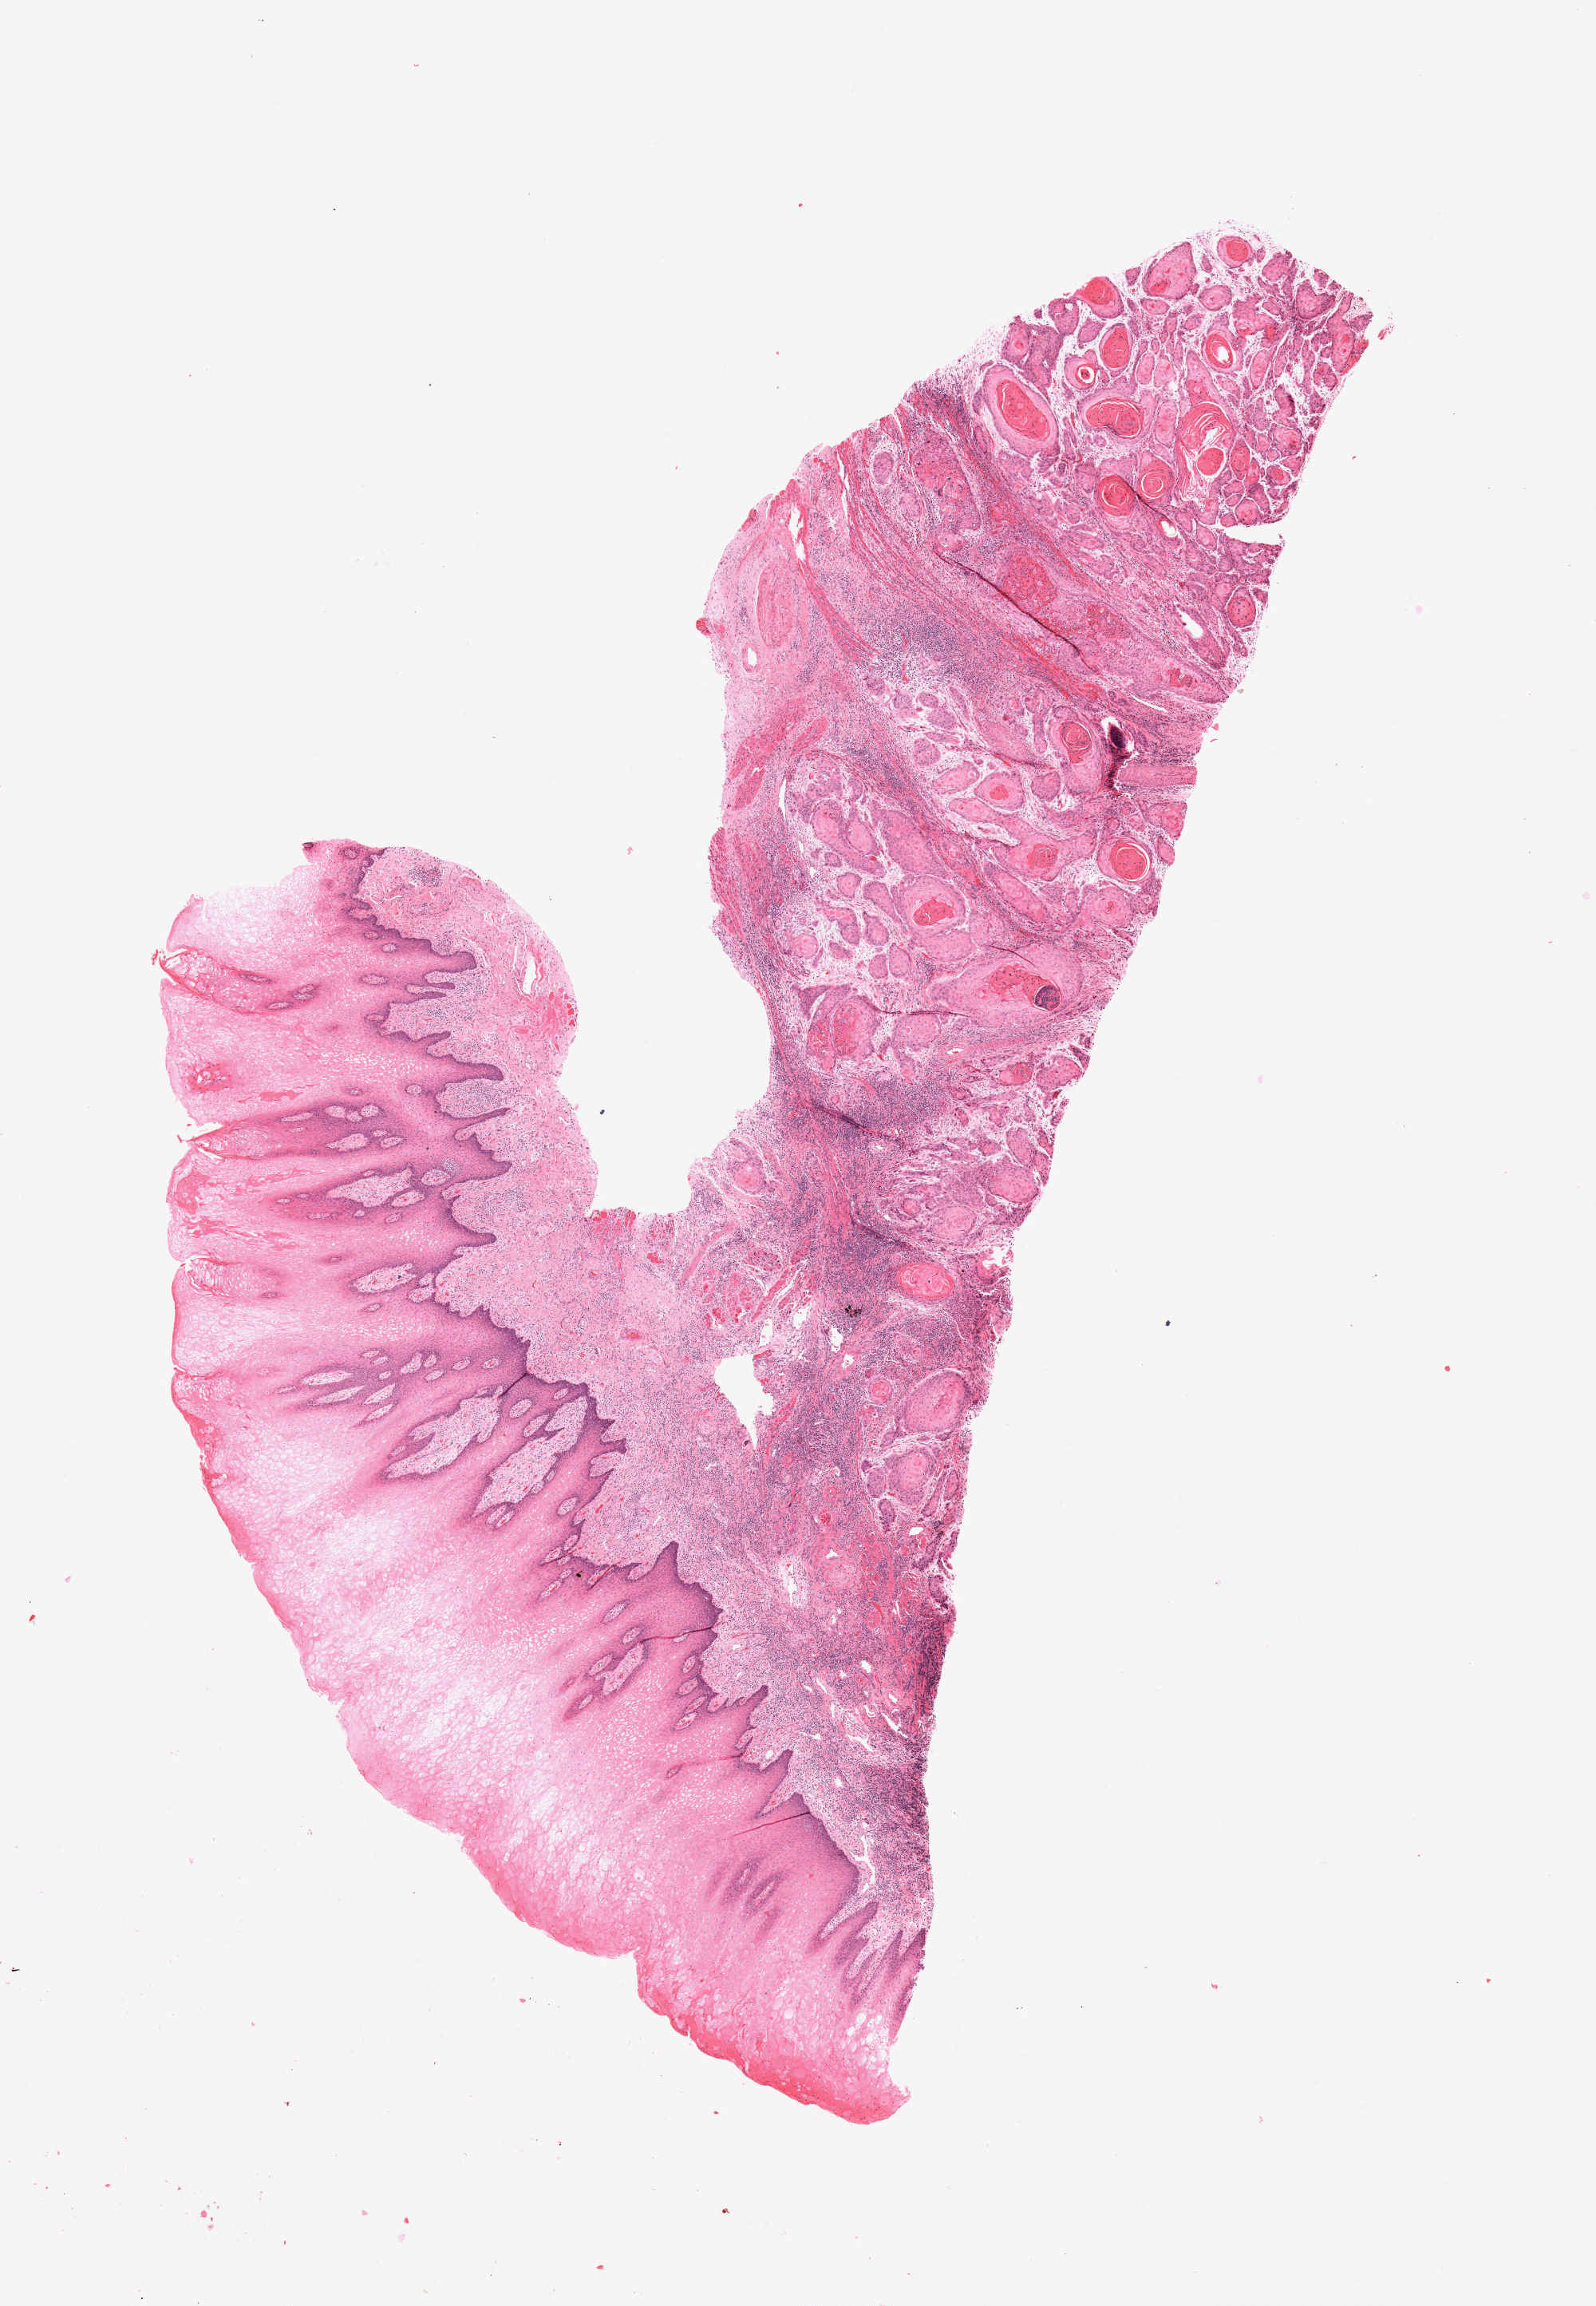
H&E-stained whole-slide image — a low-resolution overview of the entire scanned area, about 8.0 x 11.5 mm (from a 20x scan); FFPE section; sample: primary tumour, head and neck. Patient: male, age at initial diagnosis 30 years. Histologic grade: G1 (well differentiated).
Laterality: right. AJCC pathologic stage: IVA. Histologic diagnosis: Squamous cell carcinoma, keratinizing, NOS (tongue, NOS).